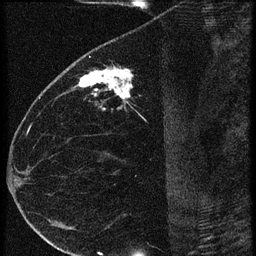
Breast MRI (dynamic contrast-enhanced), one sagittal slice. Slice 29 of 60 in the series (ordered by position). 3 images stored at this slice position (order not interpretable as contrast timing). 1.5 T. TE 4.2 ms, TR 20.4 ms. 256 × 256 image matrix, field of view 180 × 180 mm. Female patient, age 35 years. From the clinical record (not read from this slice): setting: breast cancer imaged before/during neoadjuvant chemotherapy; receptor status: HR-positive, HER2-negative.
Structures marked on this image (semi-automatic segmentation, software-assisted and operator-edited):
- analysis volume of interest (the breast-tissue region the enhancement analysis was run in; not a lesion): bounding box [x1, y1, x2, y2] px = [65, 60, 169, 119]
- tumour enhancement mask (voxels above the 90 % enhancement threshold inside the analysis volume of interest): [73, 68, 131, 101]